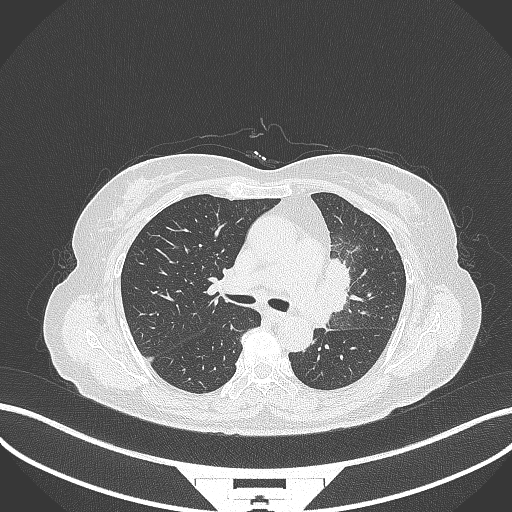
Chest CT, one axial slice; position 207 of 382 along the scan axis; reconstruction kernel B70f; lung window (W 1500 / L -600 HU); 1 mm slice thickness; 512 × 512 image matrix, field of view 400 × 400 mm. Female patient, age 64 years. Case-level facts recorded for this patient, not image findings: clinical TNM (as recorded): T2a N2 M0.
Outlined on this slice (bounding box drawn by a radiologist):
- lung tumour (recorded histology: adenocarcinoma): bounding box <317,254,363,317> (left, top, right, bottom; pixels)